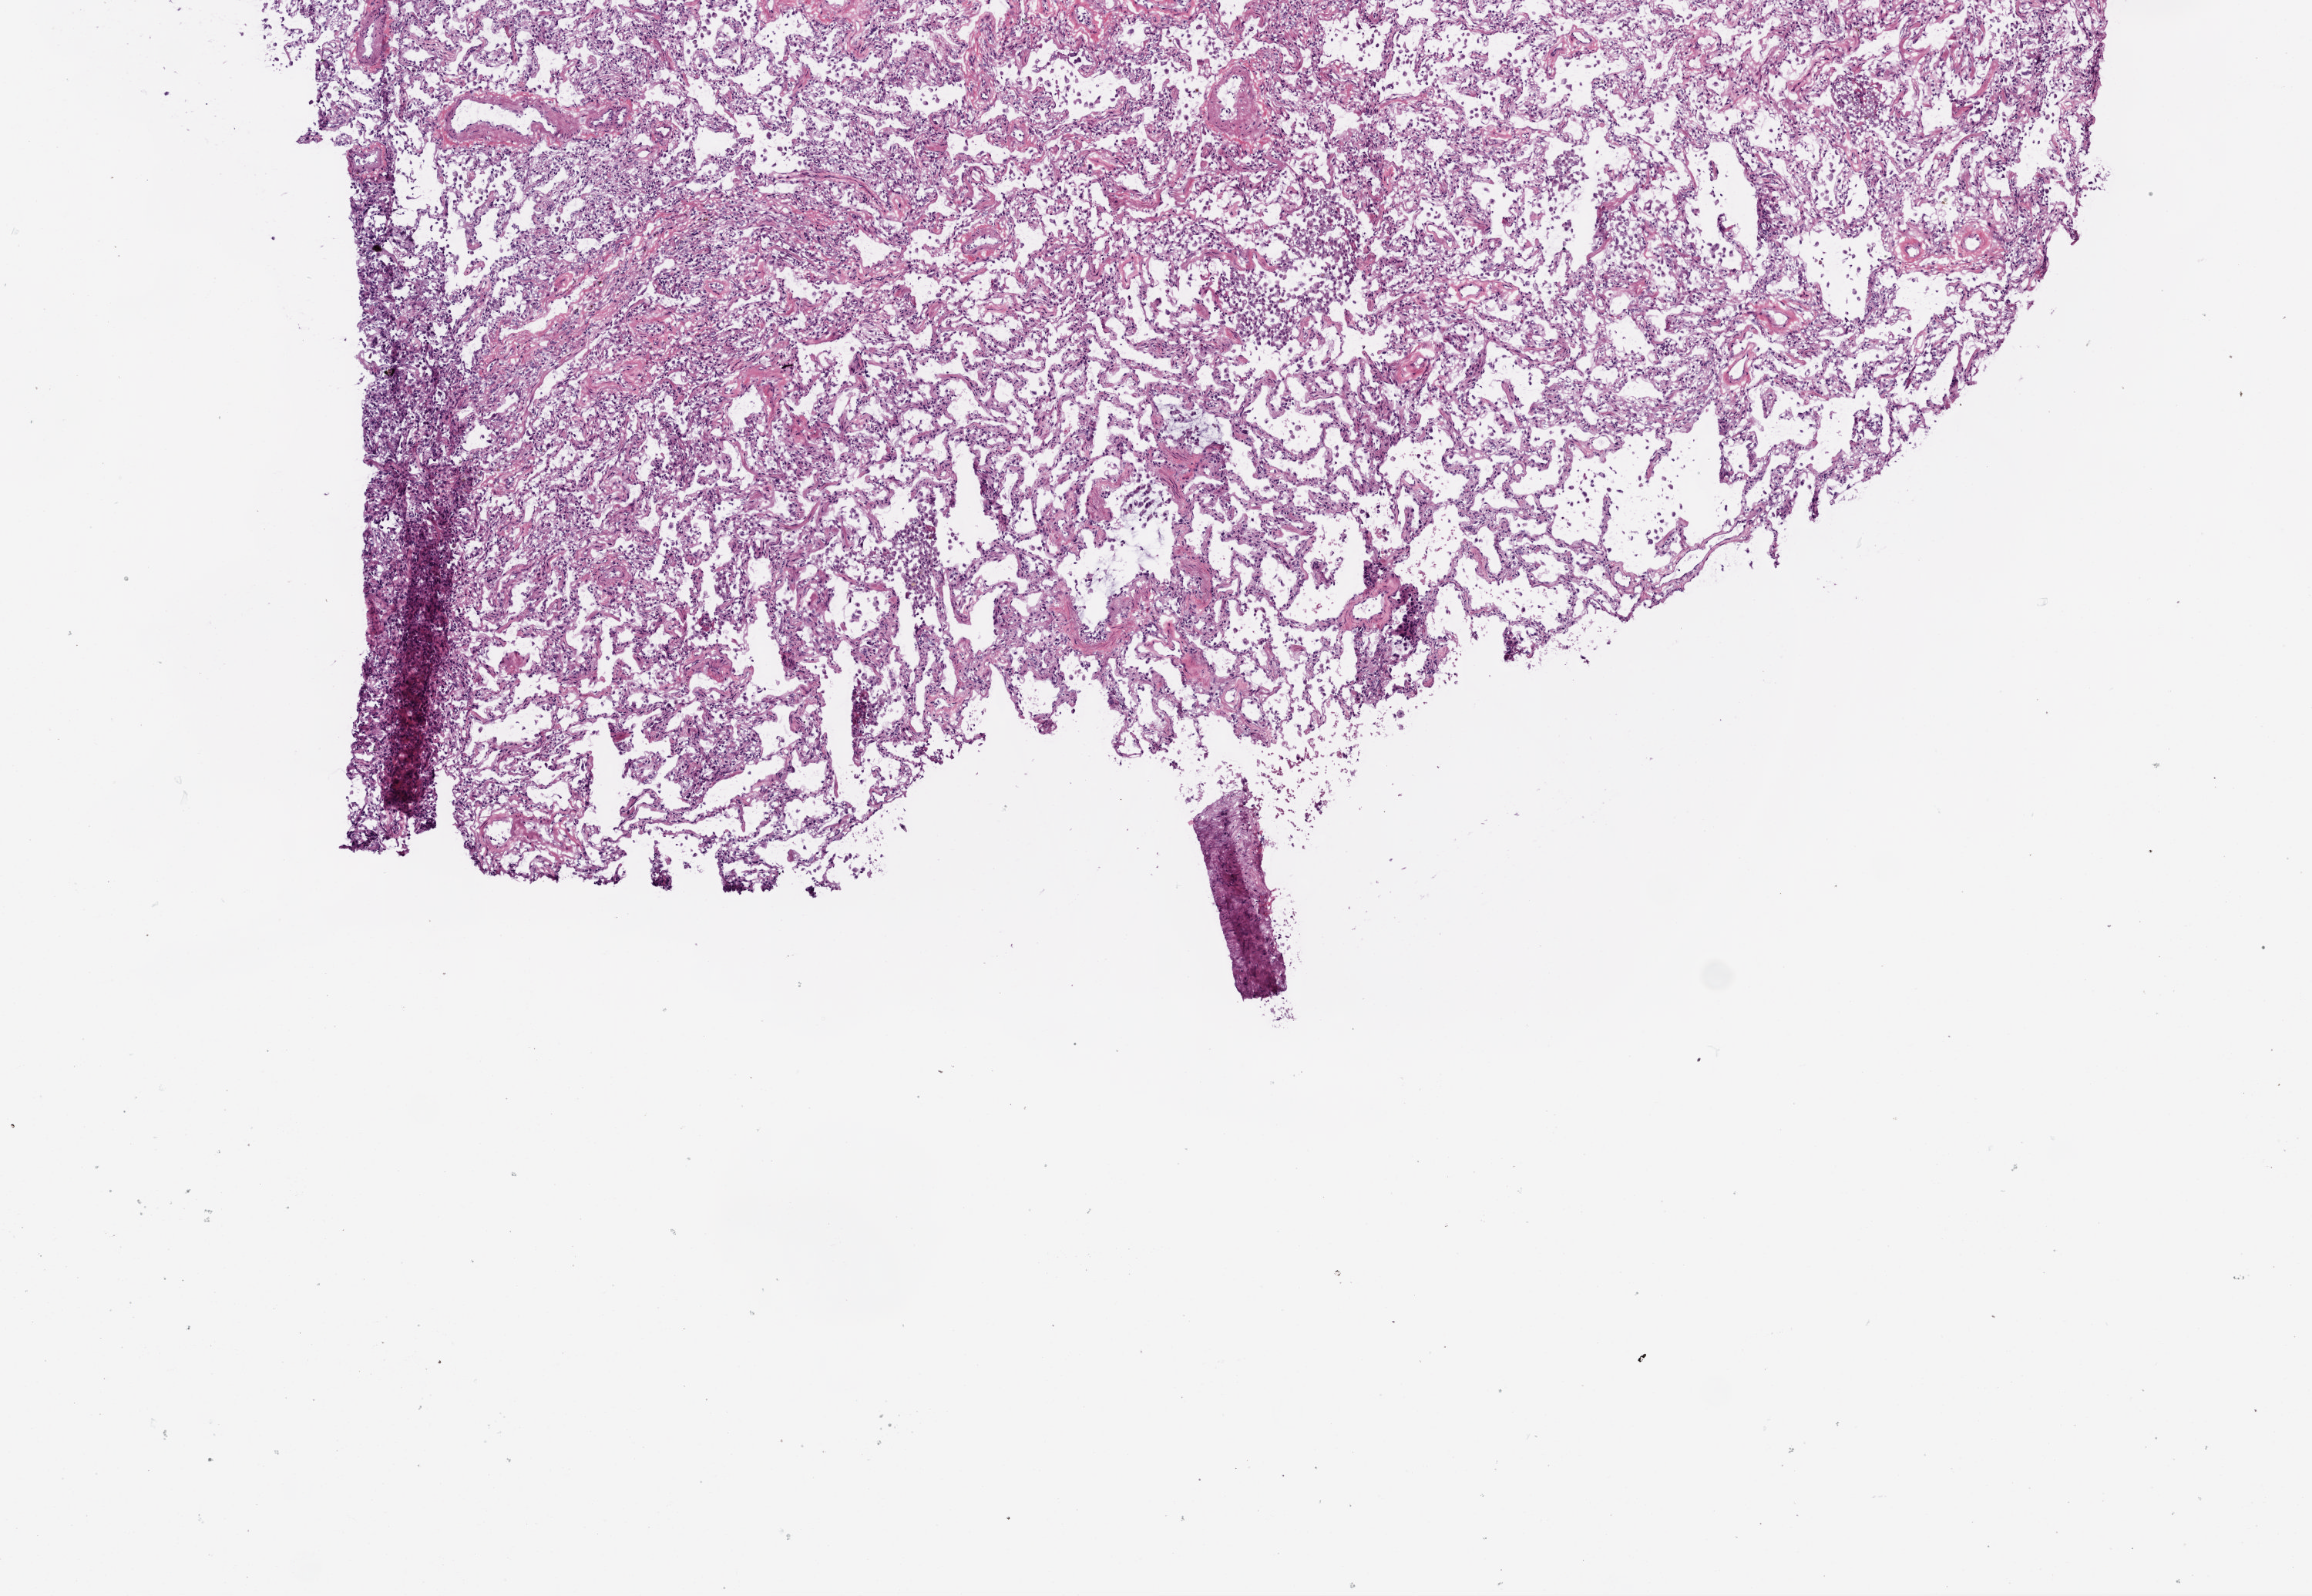
H&E-stained whole-slide image, low-resolution overview of the scanned area, about 6.0 x 4.2 mm (slide scanned at 20x), frozen section from the top of the tissue portion, lung, solid tissue normal (non-tumour tissue) sample. Female patient; age at initial diagnosis 64 years.
This section: solid tissue normal sample (biorepository sample class). Patient diagnosis: Adenocarcinoma, NOS (upper lobe, lung).